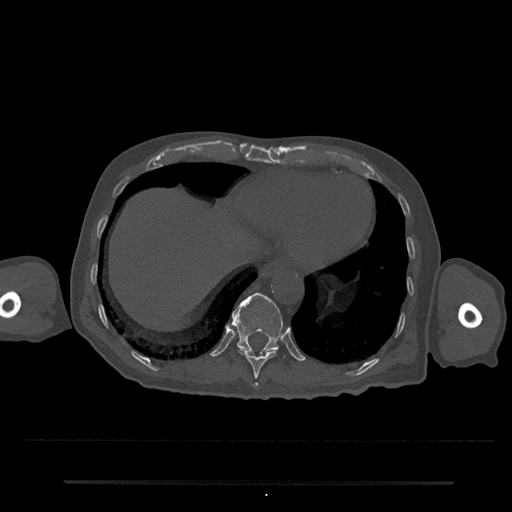
CT including the spine, one axial slice. Slice 285 of 797 in the series (ordered by position). Reconstruction kernel Br40s/3. Bone window (W 1800 / L 400 HU). 0.5 mm slice thickness. 512 × 512 image matrix, field of view 427 × 427 mm. Patient: male, 74 years. Case-level facts recorded for this patient, not image findings: primary cancer: prostate.
Outlined on this slice (semi-automatically segmented with operator editing):
- T10 vertebra: bounding box <238,349,277,387> (left, top, right, bottom; pixels)
- T11 vertebra: <231,292,283,354>